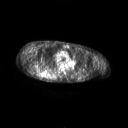
FDG PET of an extremity soft-tissue mass (from a PET/CT study), one axial slice. Position 182 of 267 along the scan axis. 128 × 128 image matrix. Male patient, age 61 years. Case-level facts recorded for this patient, not image findings: histological type: pleiomorphic spindle cell undifferentiated; grade: high; site of the primary tumour: right parascapusular.
Annotated regions visible in this slice (expert contour drawn on MRI and transferred to this co-registered scan by the dataset authors):
- gross tumour volume including surrounding oedema: bounding box [x1, y1, x2, y2] px = [34, 69, 57, 79]
- gross tumour volume (mass): [38, 69, 48, 77]